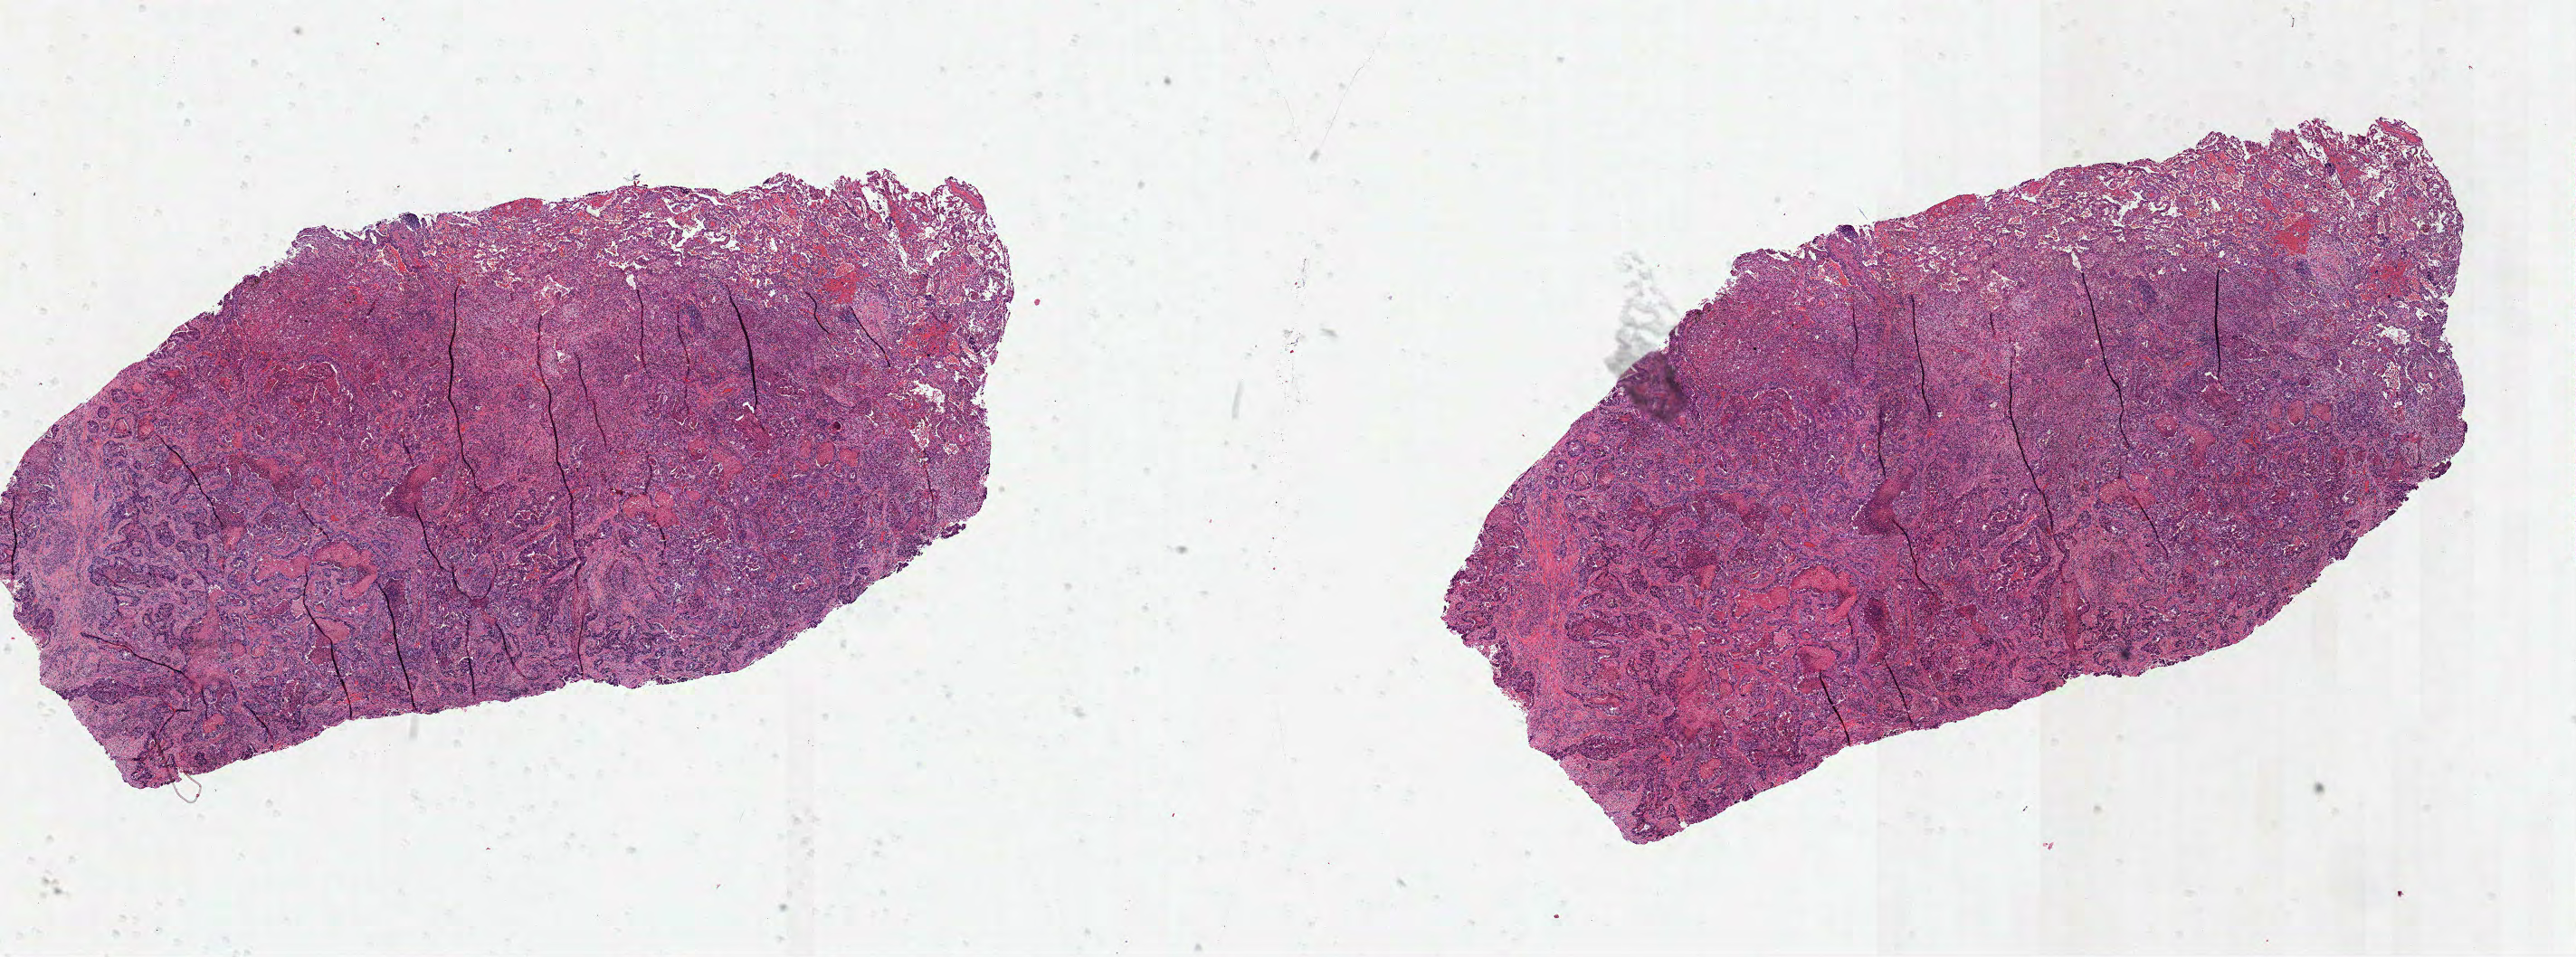
Digitized H&E-stained tissue section (whole slide), low-resolution overview of the scanned area, about 23.0 x 8.5 mm (slide scanned at 40x); FFPE section; primary tumour sample from the lung. Patient: female, age at initial diagnosis 56 years.
- pathologic diagnosis: Adenocarcinoma, NOS
- AJCC pathologic stage: IIIA (7th edition)